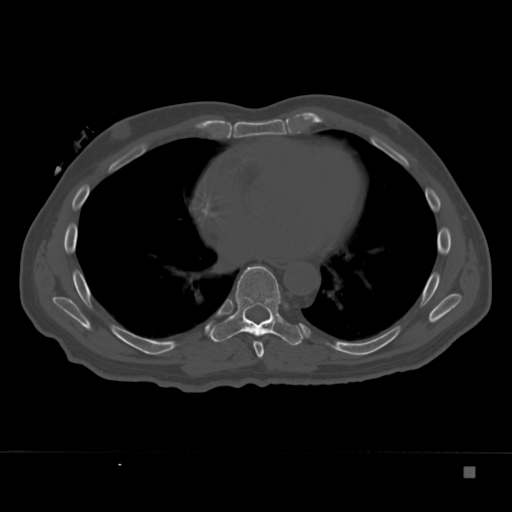
CT including the spine, one axial slice. Position 210 of 332 along the scan axis. Reconstruction kernel Br40s. 120 kVp. Bone window (W 1800 / L 400 HU). 1.5 mm slice thickness. 512 × 512 image matrix. Male patient, age 72 years. From the clinical record (not read from this slice): primary cancer: skeletal.
Structures marked on this image (semi-automatically segmented with operator editing):
- T7 vertebra: box from (x=253, y=340) to (x=265, y=358) px
- T8 vertebra: (x=210, y=266)–(x=306, y=346)